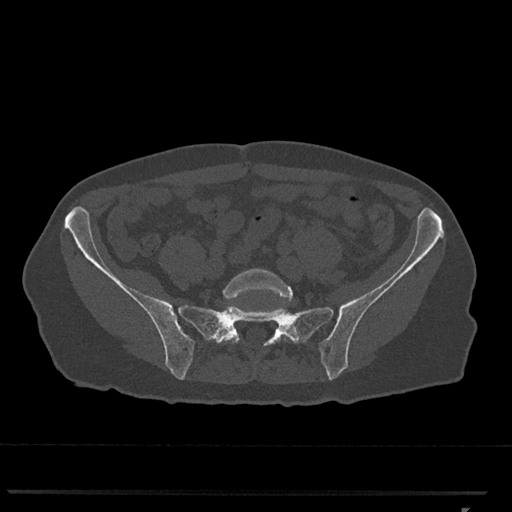
CT including the spine, one axial slice; slice 118 of 793 in the series (ordered by position); reconstruction kernel Br40s/3; bone window (W 1800 / L 400 HU); 0.5 mm slice thickness; 512 × 512 image matrix, field of view 380 × 380 mm. Female patient, age 62 years. Case-level facts recorded for this patient, not image findings: primary cancer: renal.
Annotated regions visible in this slice (semi-automatic segmentation, software-assisted and operator-edited):
- L5 vertebra: bounding box [x1, y1, x2, y2] px = [222, 269, 295, 342]